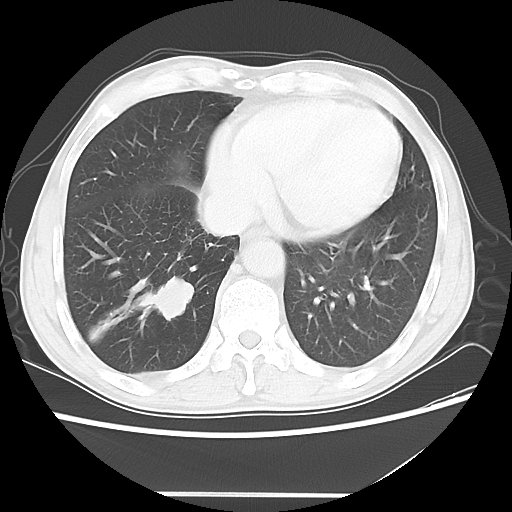
Chest CT, one axial slice; position 15 of 56 along the scan axis; reconstruction kernel LUNG; 120 kVp; lung window (W 1500 / L -600 HU); 5 mm slice thickness; 512 × 512 image matrix, field of view 344 × 344 mm. Male patient, age 65 years. From the clinical record (not read from this slice): clinical TNM (as recorded): T1c N3 M0.
Annotated regions visible in this slice (bounding box drawn by a radiologist):
- lung tumour (recorded histology: small cell carcinoma): bounding box (x1, y1, x2, y2) in pixels: (144, 274, 201, 322)